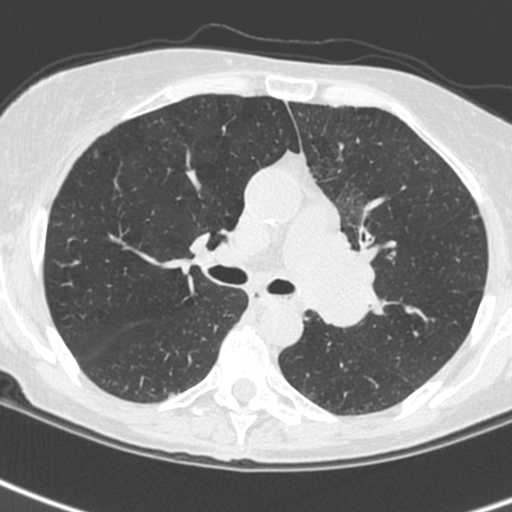
Low-dose screening chest CT, one axial slice. Slice 154 of 242 in the series (ordered by position). 120 kVp. Lung window (W 1500 / L -600 HU). 1.3 mm slice thickness. 512 × 512 image matrix, field of view 284 × 284 mm.
Annotated regions visible in this slice (expert manual segmentation):
- lesion 3 (tumor, upper lobe of left lung): bounding box [x1, y1, x2, y2] px = [312, 203, 376, 328]